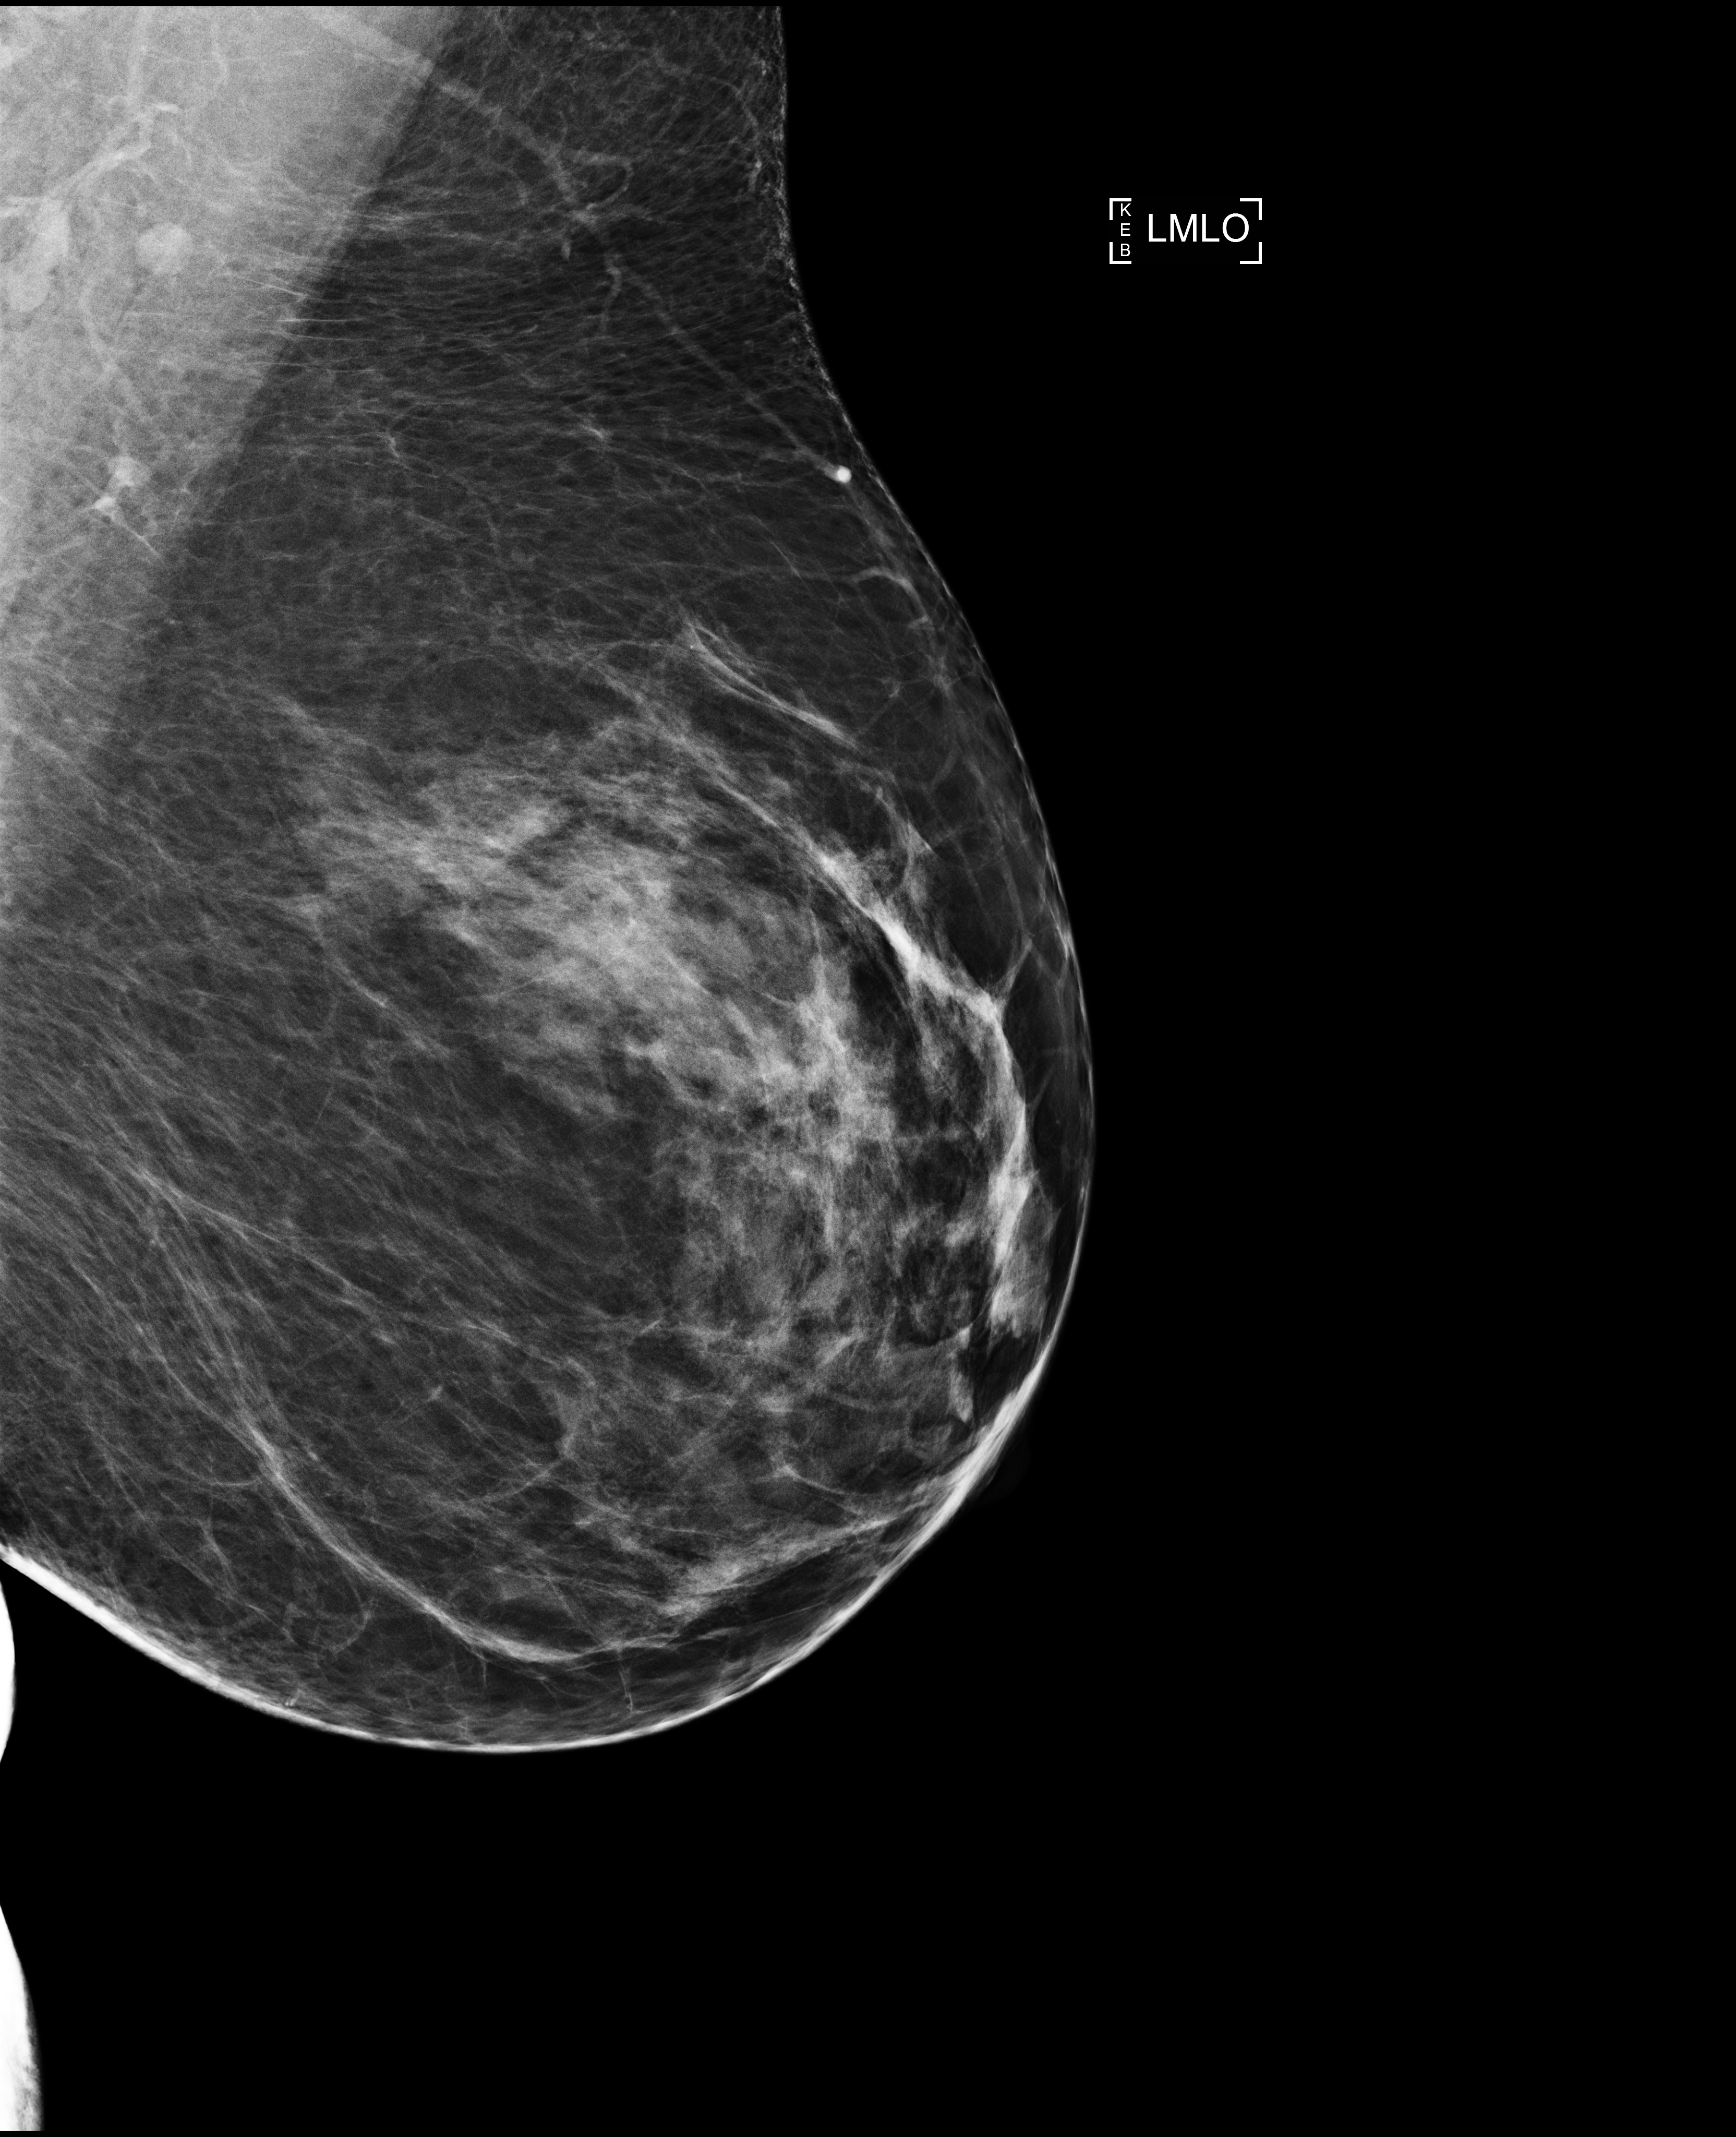
Screening examination, system: Selenia Dimensions. Patient: female, 64 years.
Image type: full-field digital mammogram. Breast: left. Projection: MLO view.